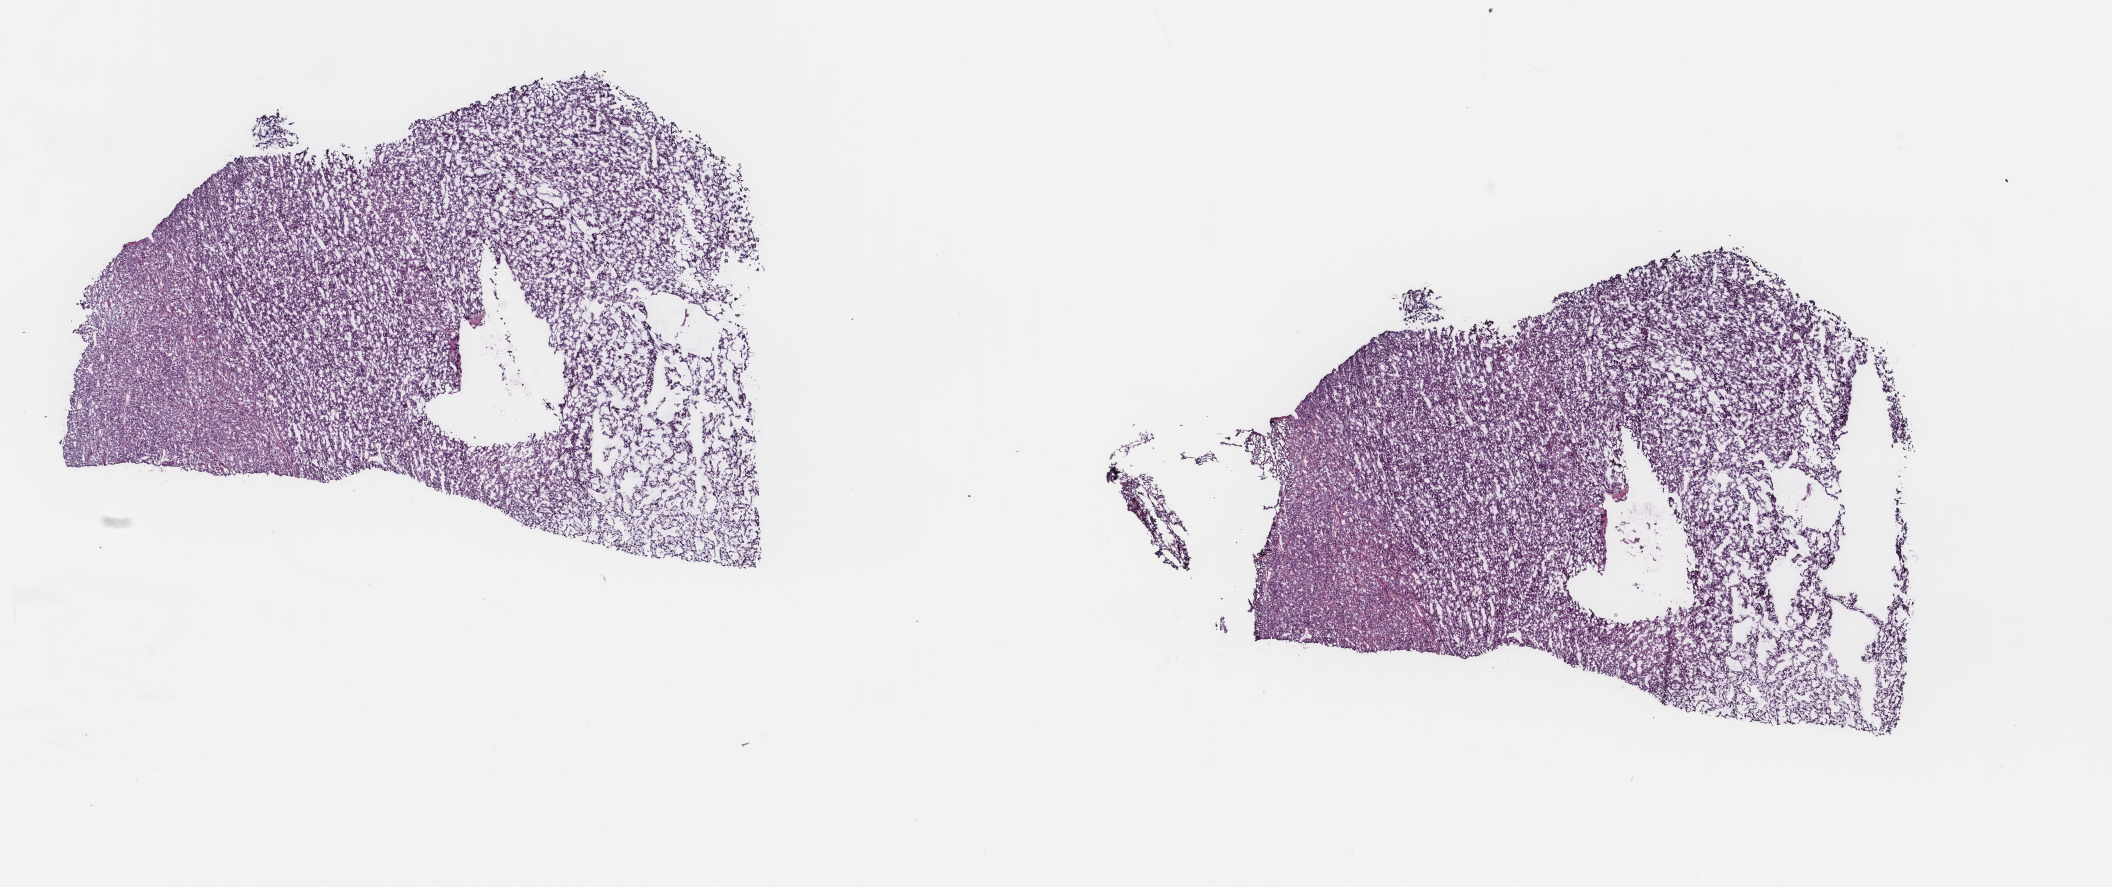
Hematoxylin and eosin (H&E) stained whole-slide image, low-resolution overview of the scanned area, about 16.8 x 7.0 mm. Frozen section. Primary tumour sample from the adrenal cortex. Male patient; age at initial diagnosis 50 years. Composition of this section per pathologist review: tumour cells 95%, tumour nuclei 100%, normal cells 0%, stromal cells 5%, necrosis 0%. Infiltration values recorded for this section: lymphocyte infiltration 0%, monocyte infiltration 0%, neutrophil infiltration 0%.
Lymph nodes positive (case pathology): 0 of 1 examined. Laterality: left. Diagnosis: Adrenal cortical carcinoma (cortex of adrenal gland).